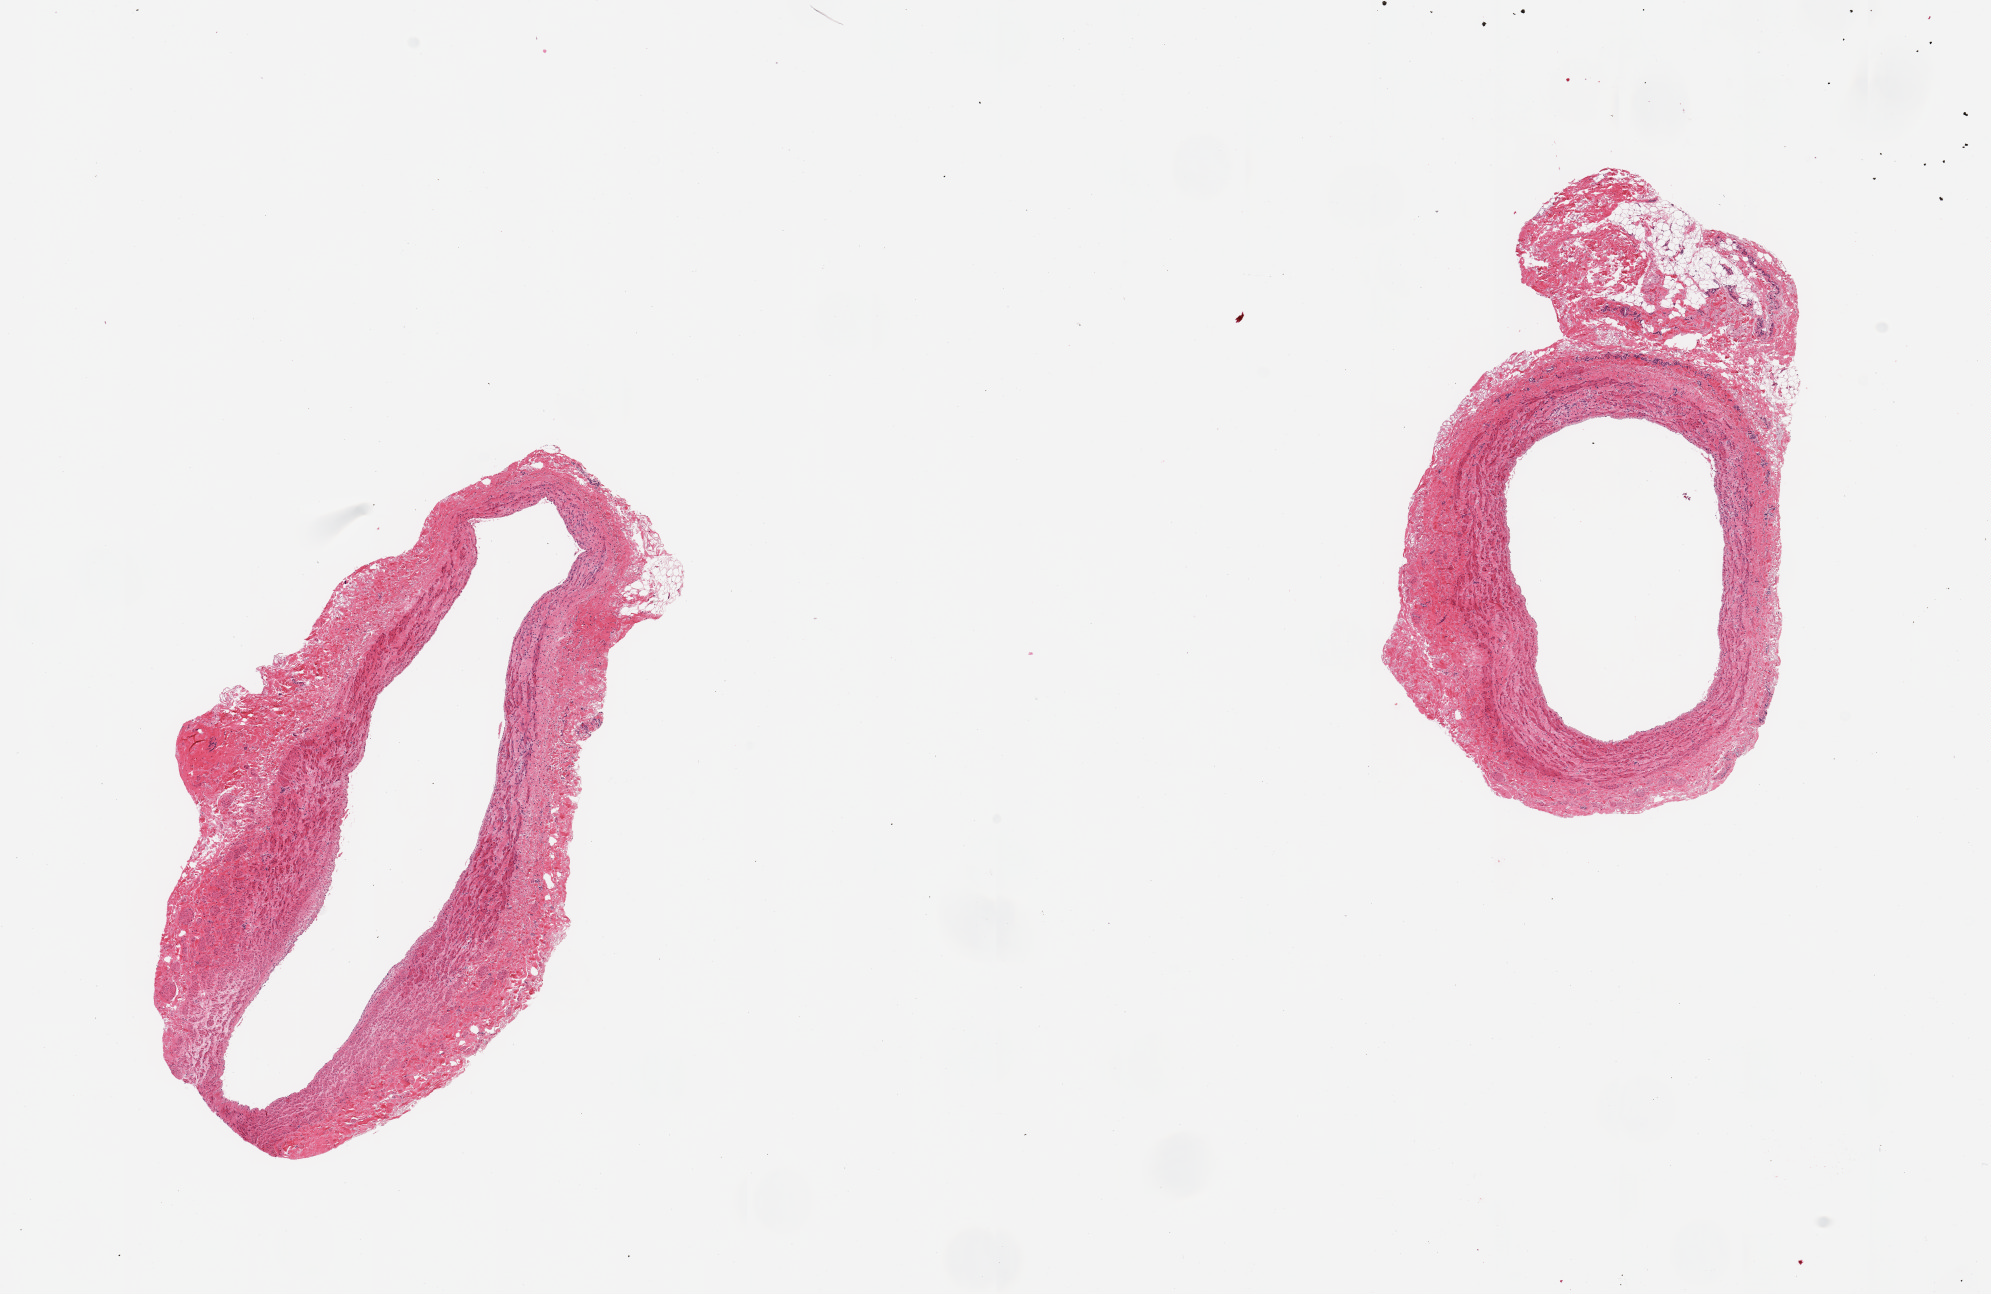
Whole-slide image, haematoxylin and eosin stain, low-resolution overview of the scanned area, about 15.8 x 10.2 mm (slide scanned at 20x), PAXgene-fixed paraffin-embedded (PFPE) section, sampled site (target tissue): tibial artery, donor tissue sample. Male donor.
Reviewer comment on this tissue sample: 2 pieces muscular artery, no atherosis, adherent nubbin fibrofatty tissue, ~1mm.